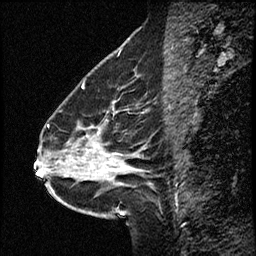
Breast MRI (dynamic contrast-enhanced), one sagittal slice. Position 23 of 50 along the scan axis. Dynamic contrast-enhanced study with each time point stored as its own series, time point 2 of 4 at this slice position (early post-contrast, ordered by acquisition time). 1.5 T. TE 4.2 ms, TR 17.5 ms. 3 mm slice thickness. 256 × 256 image matrix, field of view 200 × 200 mm. Case-level facts recorded for this patient, not image findings: setting: breast cancer imaged before/during neoadjuvant chemotherapy.
Structures marked on this image (semi-automatically segmented with operator editing):
- analysis volume of interest (the breast-tissue region the enhancement analysis was run in; not a lesion): box from (x=52, y=98) to (x=155, y=207) px
- tumour enhancement mask (voxels above the 100 % enhancement threshold inside the analysis volume of interest): (x=96, y=145)–(x=119, y=171)